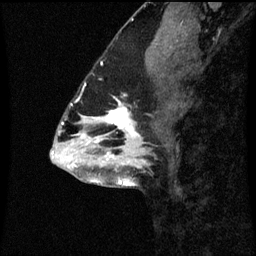
Breast MRI (dynamic contrast-enhanced), one sagittal slice. Slice 30 of 60 in the series (ordered by position). Dynamic contrast-enhanced series, image 2 of 3 at this slice position (ordered by acquisition). 1.5 T. TE 4.2 ms, TR 8.9 ms. 2 mm slice thickness. 256 × 256 image matrix, field of view 200 × 200 mm. Patient: female, 43 years. Case-level facts recorded for this patient, not image findings: setting: breast cancer imaged before/during neoadjuvant chemotherapy; receptor status: HR-positive, HER2-negative.
Annotated regions visible in this slice (semi-automatic segmentation, software-assisted and operator-edited):
- analysis volume of interest (the breast-tissue region the enhancement analysis was run in; not a lesion): bounding box (x1, y1, x2, y2) in pixels: (96, 100, 149, 159)
- tumour enhancement mask (voxels above the 70 % enhancement threshold inside the analysis volume of interest): (106, 100, 139, 157)